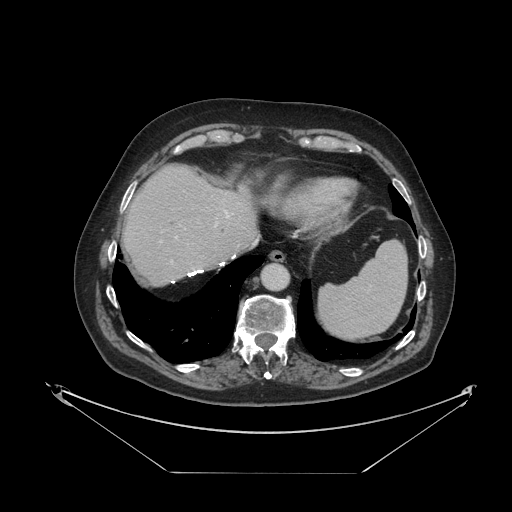
Contrast-enhanced abdominal CT, one axial slice. Position 99 of 121 along the scan axis. Reconstruction kernel STANDARD. 120 kVp. Intravenous contrast given. Soft-tissue window (W 400 / L 40 HU). 2.5 mm slice thickness. 512 × 512 image matrix, field of view 500 × 500 mm. Male patient, age 68 years. Case-level facts recorded for this patient, not image findings: diagnosis: colorectal cancer liver metastases, imaged before liver resection; multiple liver metastases: no; largest metastasis: 4 cm; disease in both lobes: no.
Annotated regions visible in this slice (expert manual segmentation):
- hepatic veins: bounding box (x1, y1, x2, y2) in pixels: (176, 212, 233, 238)
- liver: (124, 166, 256, 284)
- planned liver remnant (the part of the liver to remain after resection): (124, 166, 257, 285)
- portal vein (with intrahepatic branches): (159, 222, 218, 263)